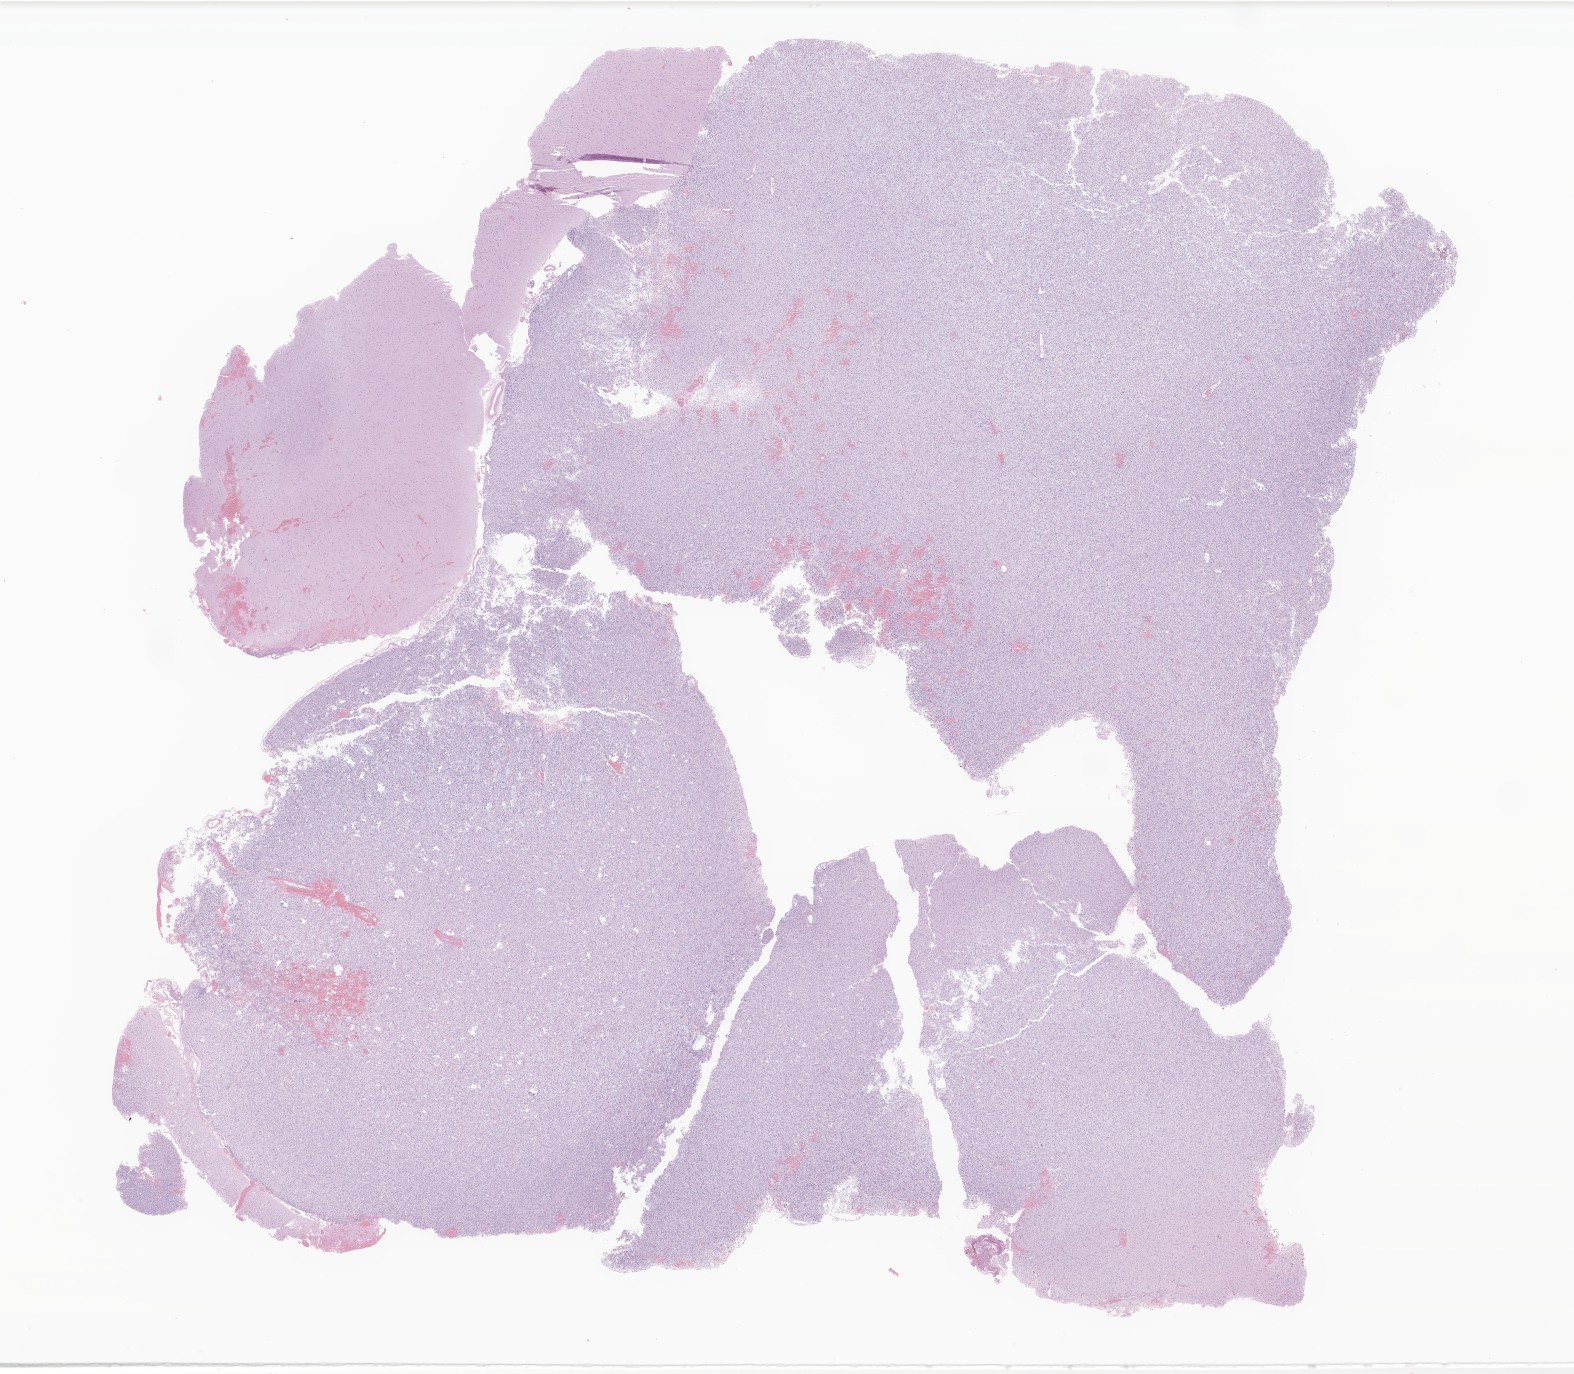
Whole-slide image, H&E stain of tumor tissue from the brain — a low-resolution overview of the entire scanned area, about 26.6 x 23.2 mm. FFPE section. Patient male; age 137 months (11 years 5 months).
* diagnosis (ICD-O-3 morphology term): Neoplasm, uncertain whether benign or malignant